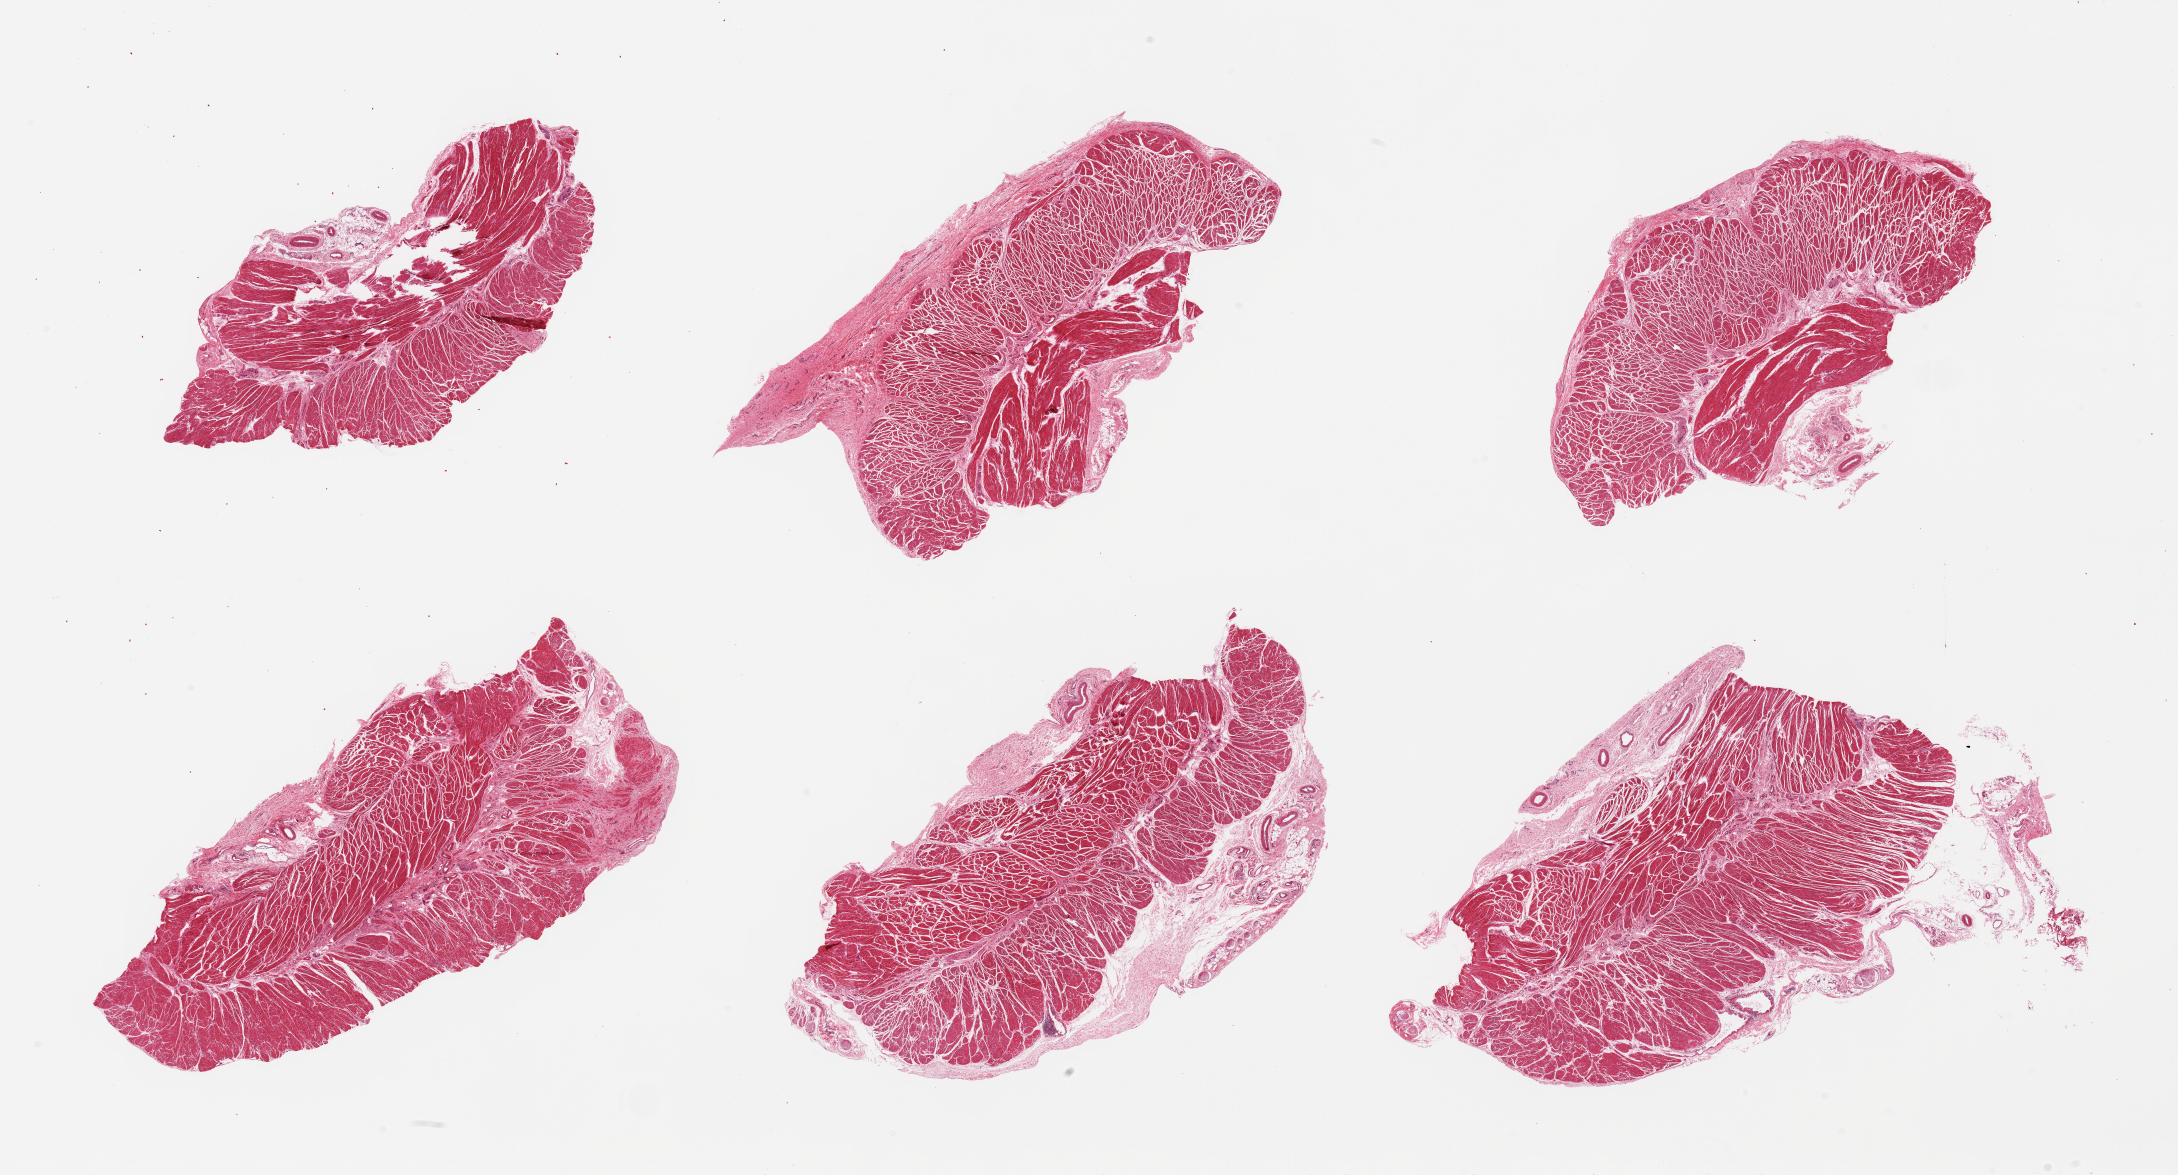
Hematoxylin and eosin (H&E) whole-slide image — whole scanned area (about 34.5 x 18.6 mm) shown as a low-resolution overview. PAXgene-fixed paraffin-embedded (PFPE) section. Target tissue: gastroesophageal junction. Tissue donor sample.
• review note (as recorded): 6 pieces; mainly muscle